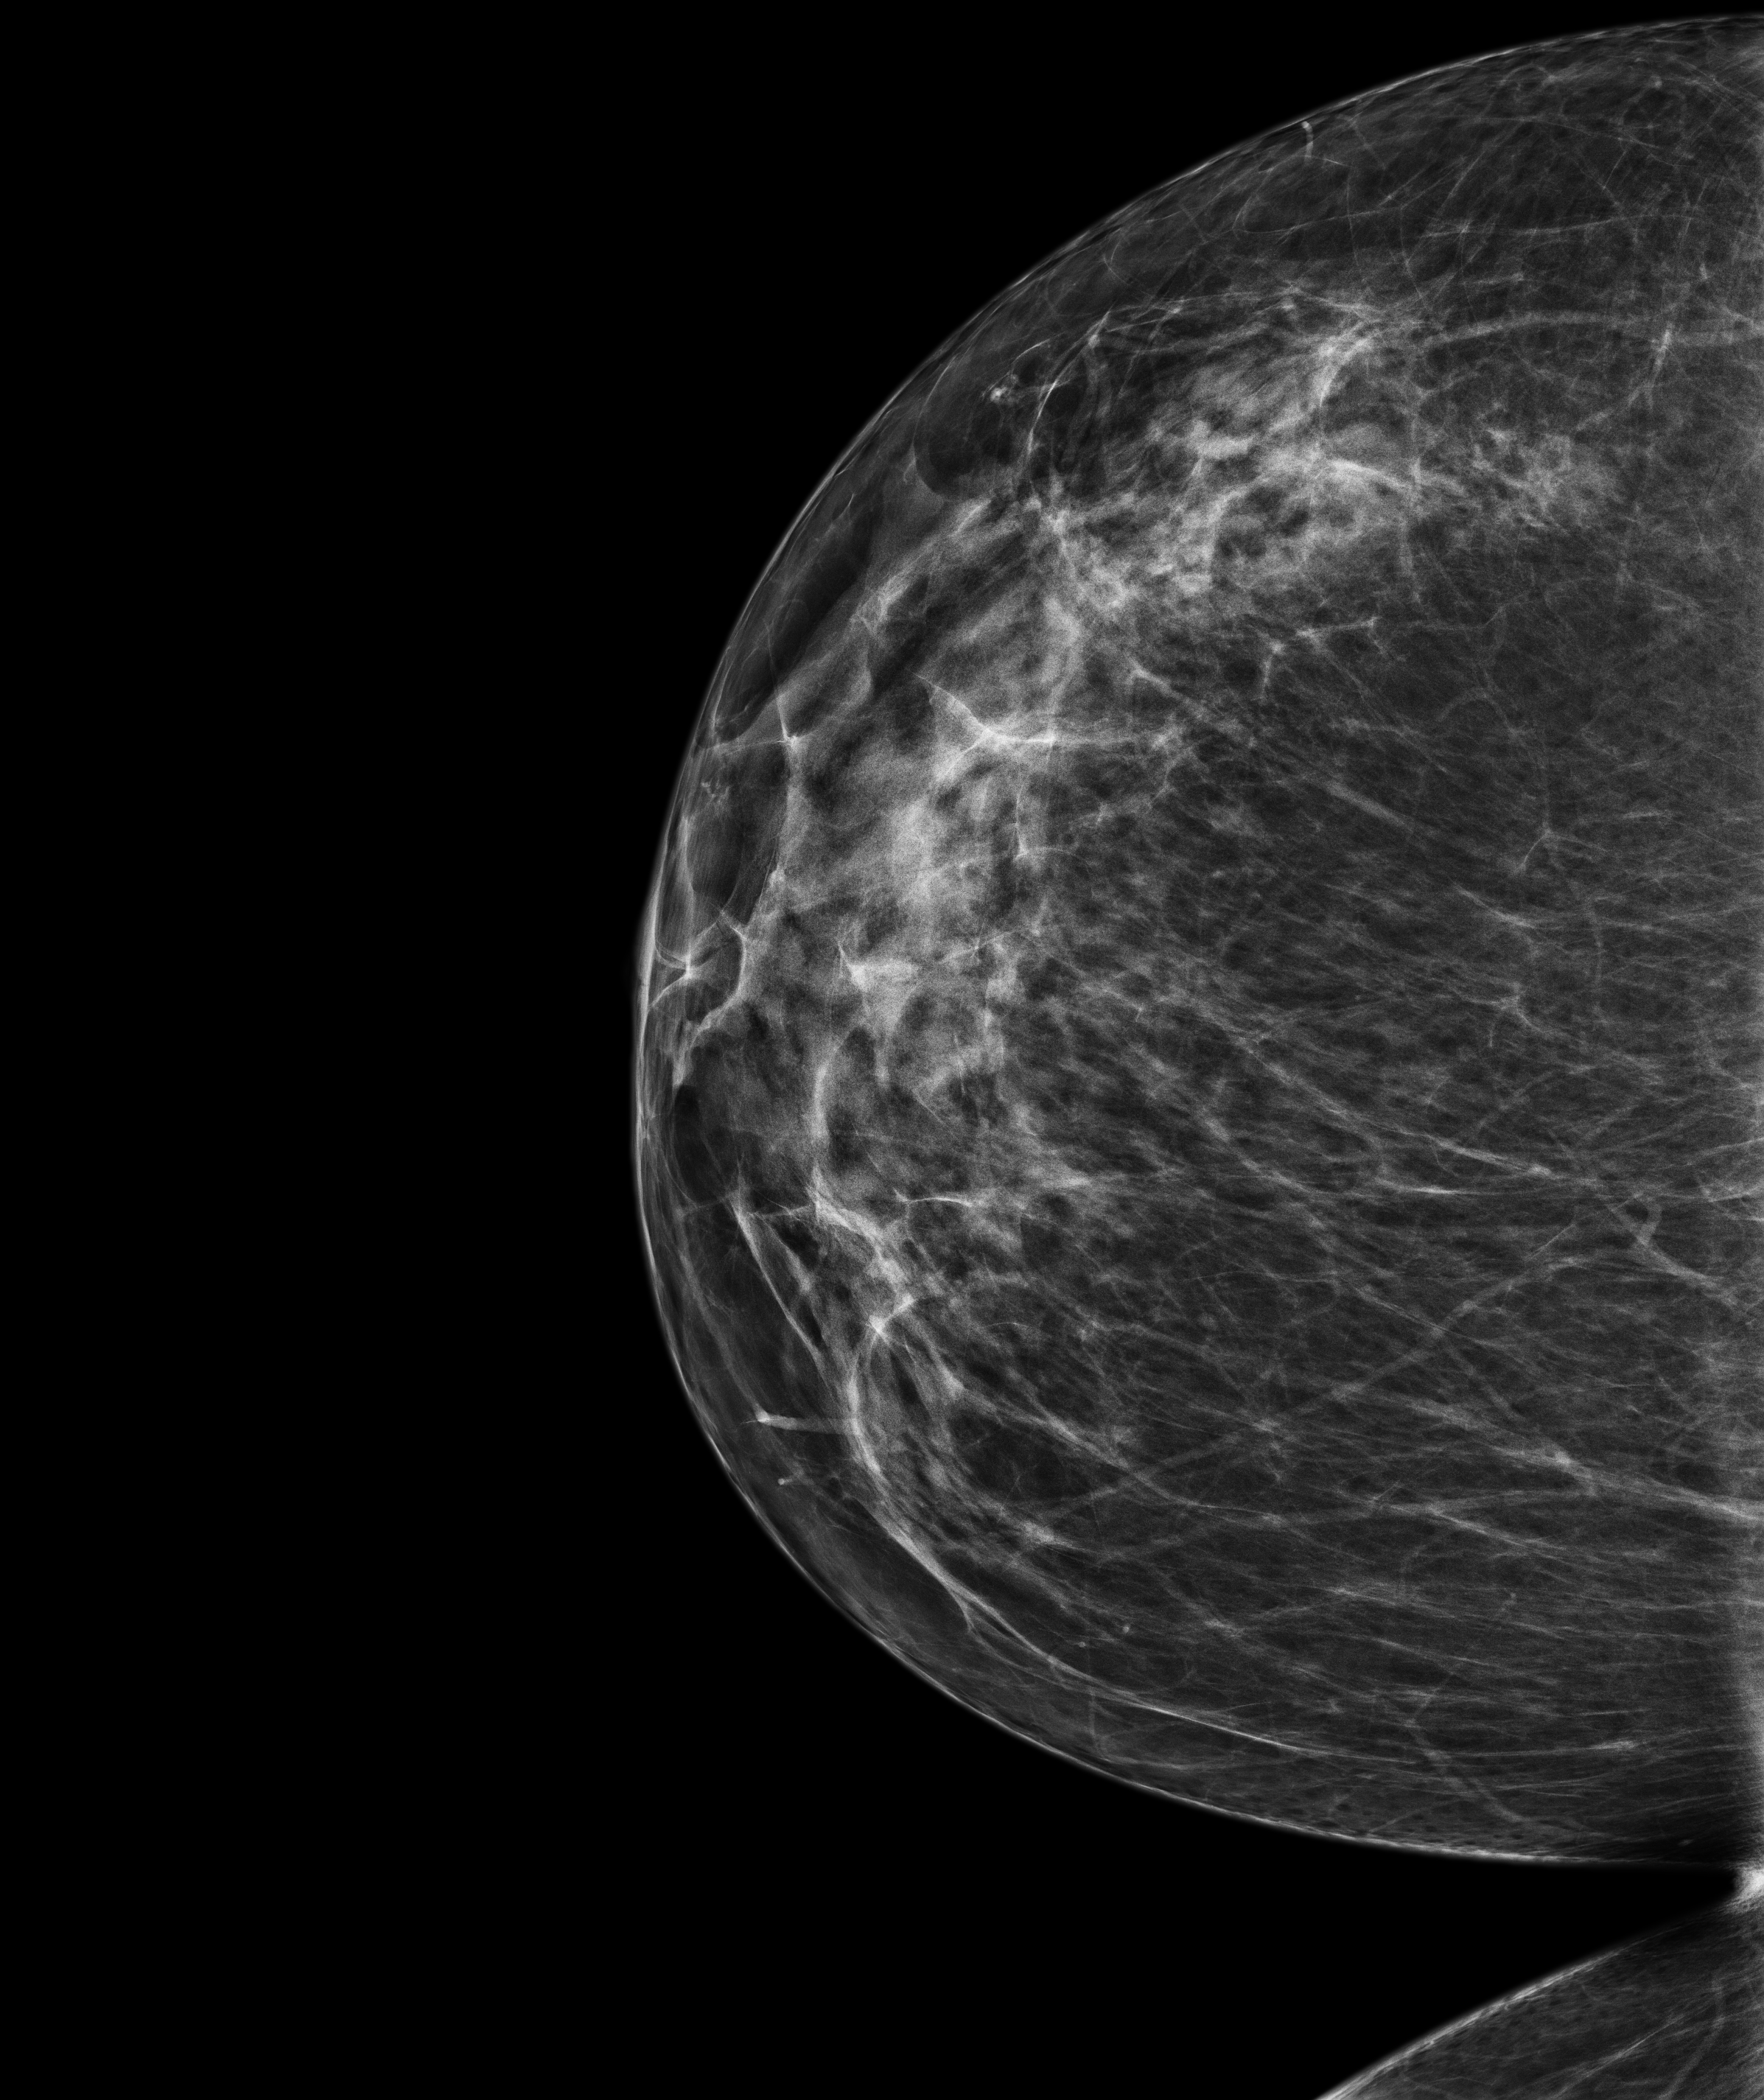
Annual screening mammography examination. Patient: female, 57 years.
Image type: full-field digital mammogram. Breast: right. Projection: craniocaudal (CC) view.